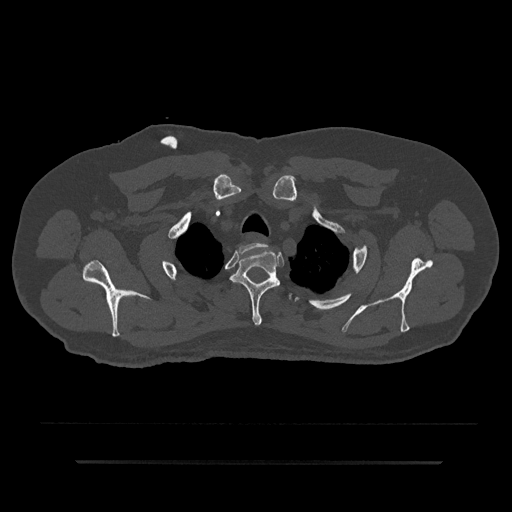
CT including the spine, one axial slice. Slice 697 of 797 in the series (ordered by position). Reconstruction kernel Br40s/3. Bone window (W 1800 / L 400 HU). 512 × 512 image matrix, field of view 464 × 464 mm. Patient: male, 59 years. Case-level facts recorded for this patient, not image findings: primary cancer: bile ducts; vertebrae with lytic lesions (as recorded): T10.
Structures marked on this image (semi-automatic segmentation, software-assisted and operator-edited):
- T1 vertebra: bounding box [x1, y1, x2, y2] px = [239, 243, 268, 254]
- T2 vertebra: [230, 251, 280, 326]
- T3 vertebra: [289, 293, 292, 300]